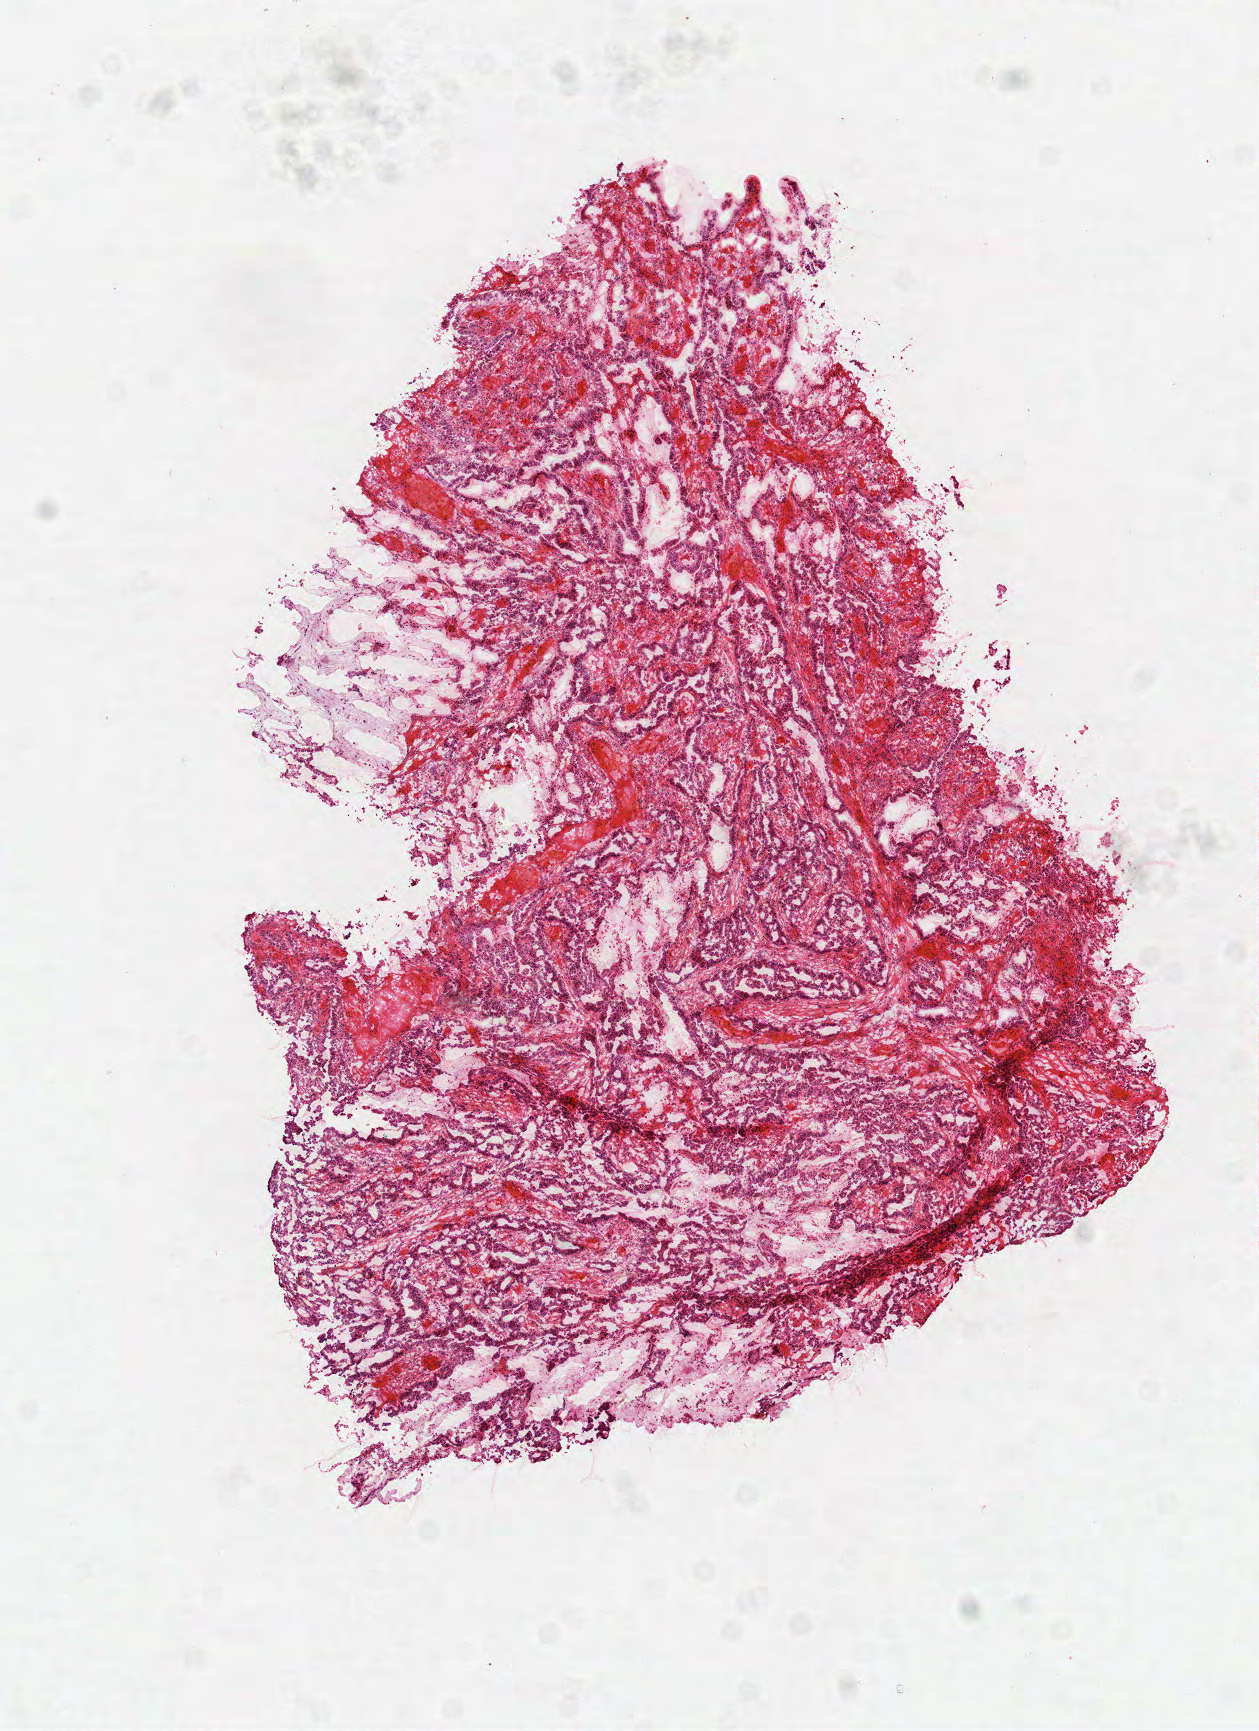
Whole-slide histology image, Hematoxylin and eosin (H&E) stained, a low-resolution overview of the entire scanned area, about 5.1 x 7.0 mm (slide scanned at 40x), frozen section from the top of the tissue portion, primary tumour sample from the colon. Patient: female, age at initial diagnosis 58 years. Pathologist review of this section (percent, as recorded): tumour cells 78%, tumour nuclei 80%, normal cells 0%, stromal cells 20%, necrosis 2%.
Histologic diagnosis: Adenocarcinoma, NOS (ascending colon). AJCC pathologic stage: IIA (6th edition).